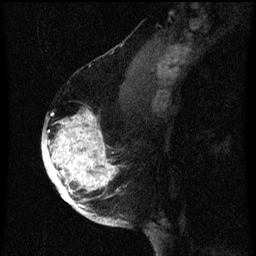
Breast MRI (dynamic contrast-enhanced), one sagittal slice; dynamic contrast-enhanced series, image 2 of 3 at this slice position (ordered by acquisition); 1.5 T; TE 4.2 ms, TR 8 ms; 2 mm slice thickness; 256 × 256 image matrix, field of view 180 × 180 mm. Female patient, age 56 years.
Annotated regions visible in this slice (semi-automatic segmentation, software-assisted and operator-edited):
- analysis volume of interest (the breast-tissue region the enhancement analysis was run in; not a lesion): box from (x=42, y=114) to (x=125, y=219) px
- tumour enhancement mask (voxels above the 70 % enhancement threshold inside the analysis volume of interest): (x=42, y=114)–(x=119, y=219)